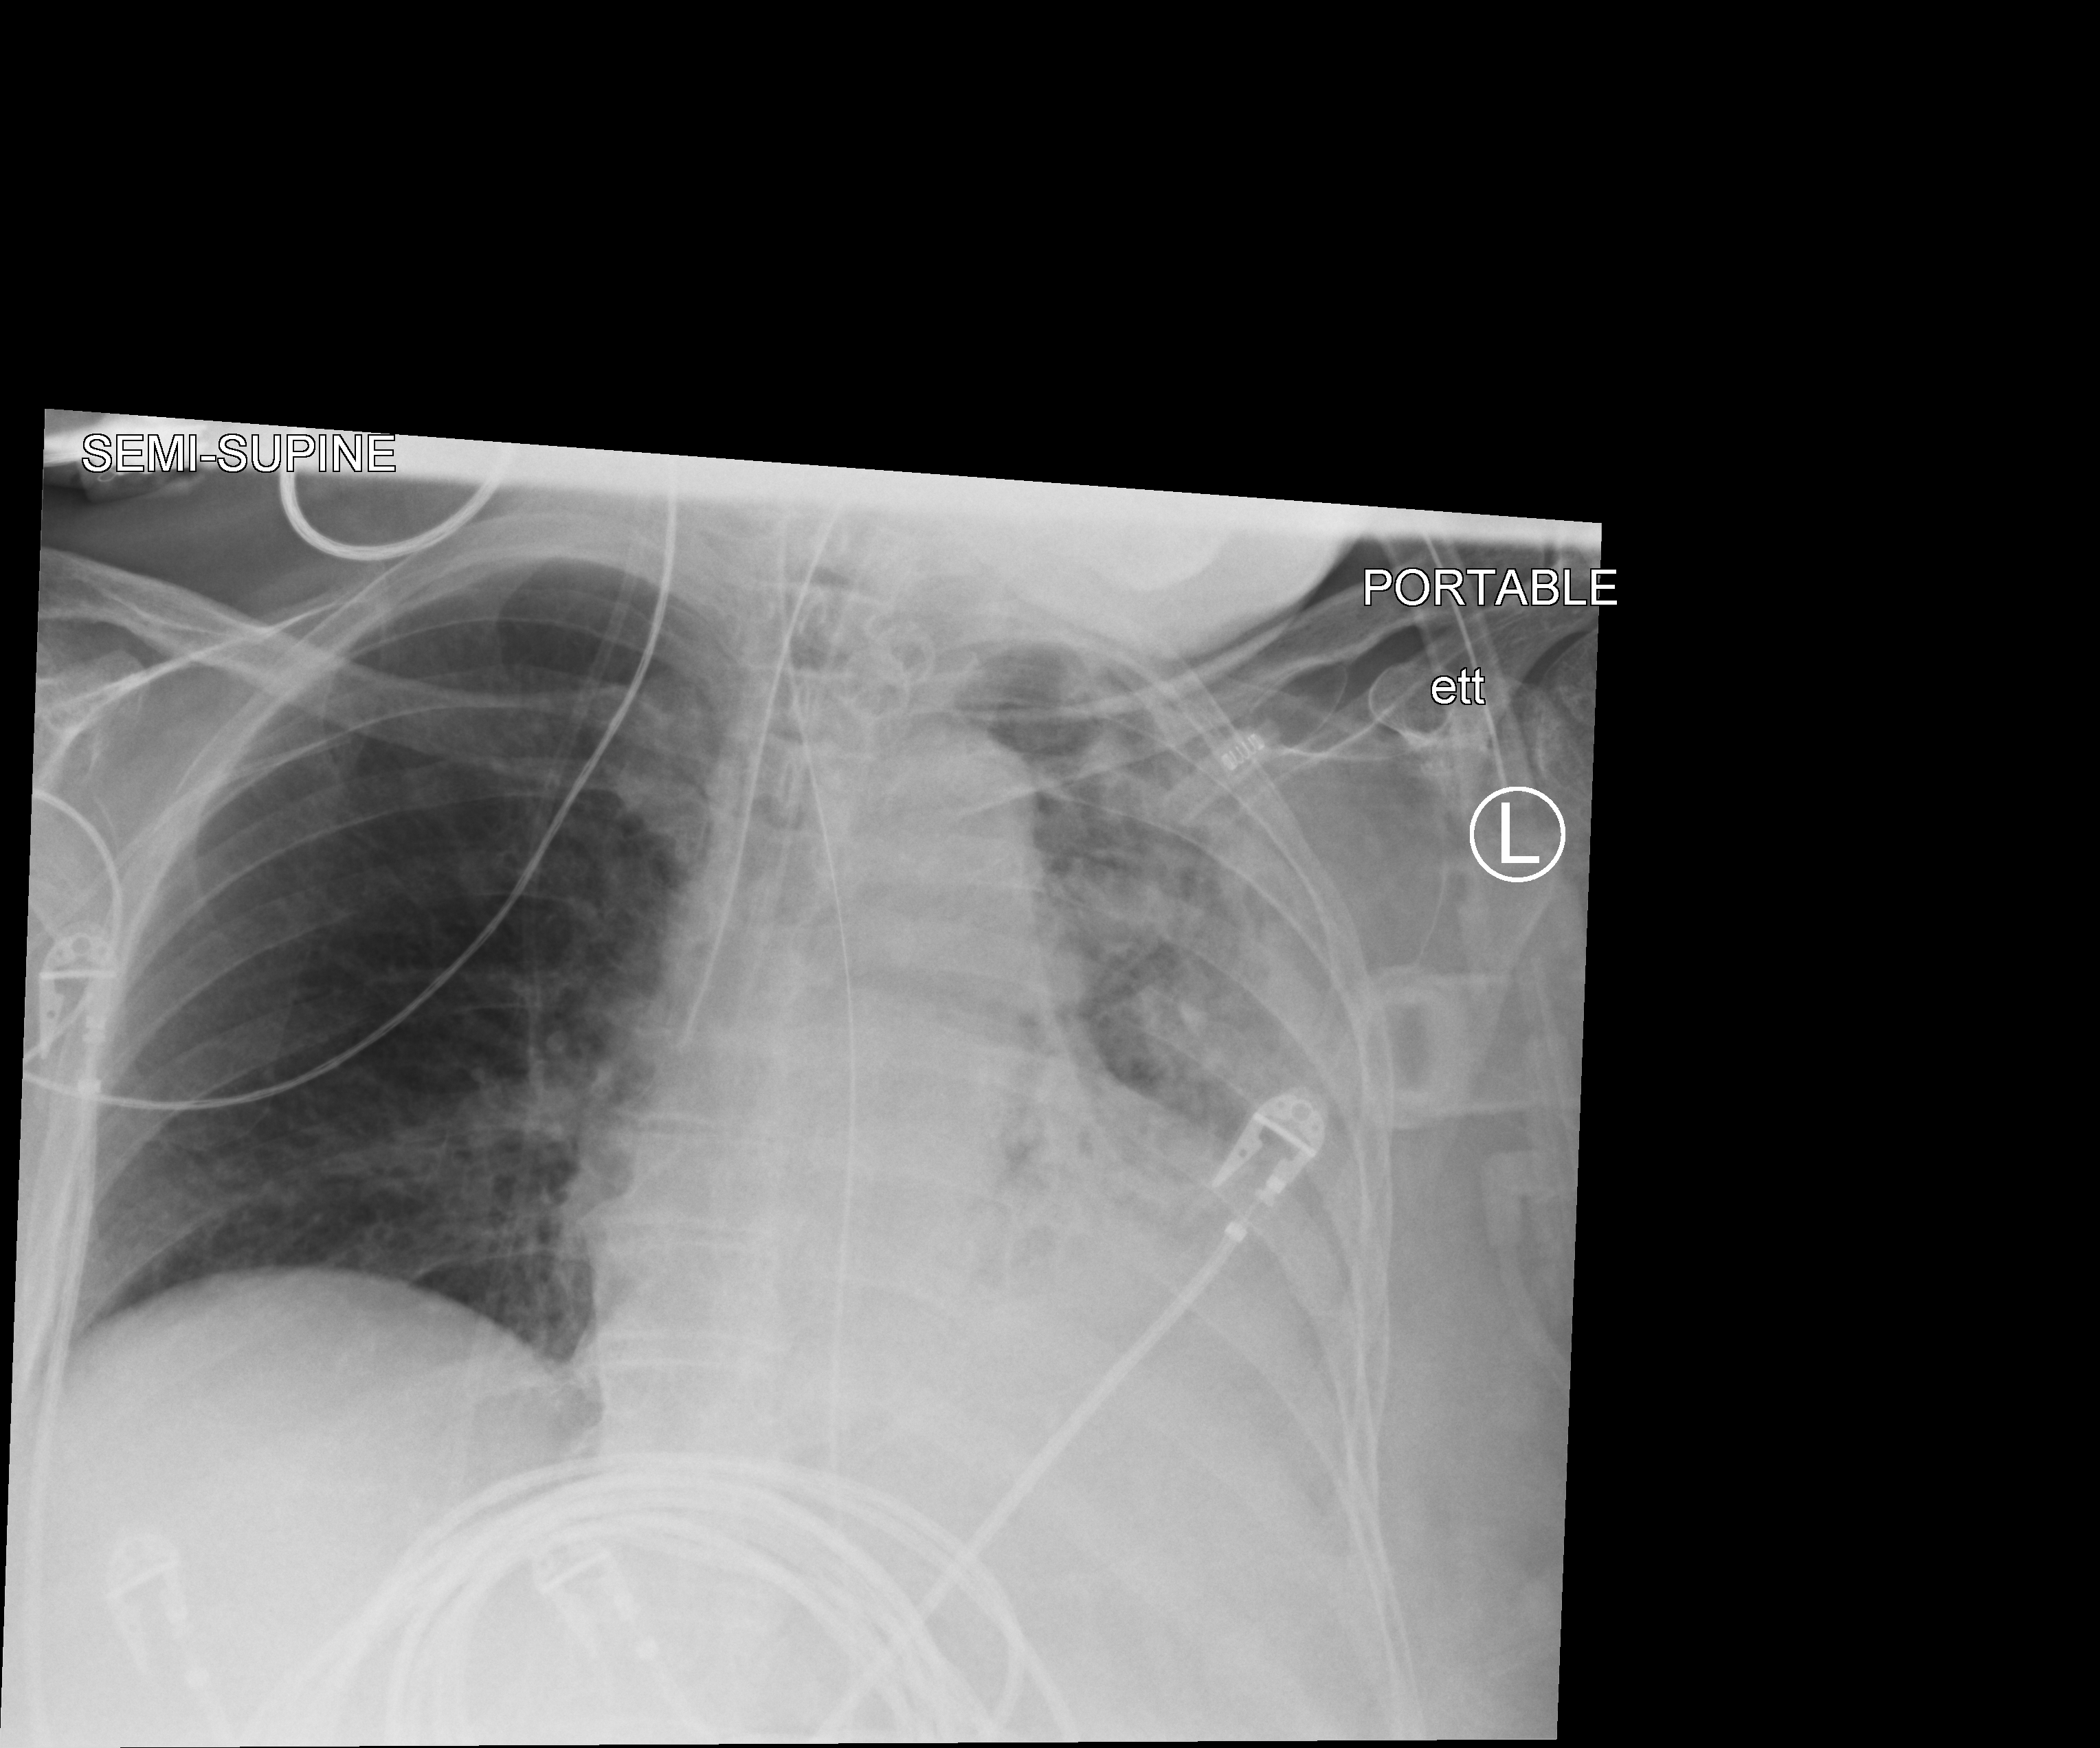
Chest X-ray (portable), anteroposterior (AP) projection. Patient hospitalised with COVID-19; female, aged 75–90 years.
Hospital-stay facts (about this admission, not read from this image; timing relative to this image not recorded): mechanically ventilated during this hospital stay: yes; admitted to intensive care during this hospital stay: yes.